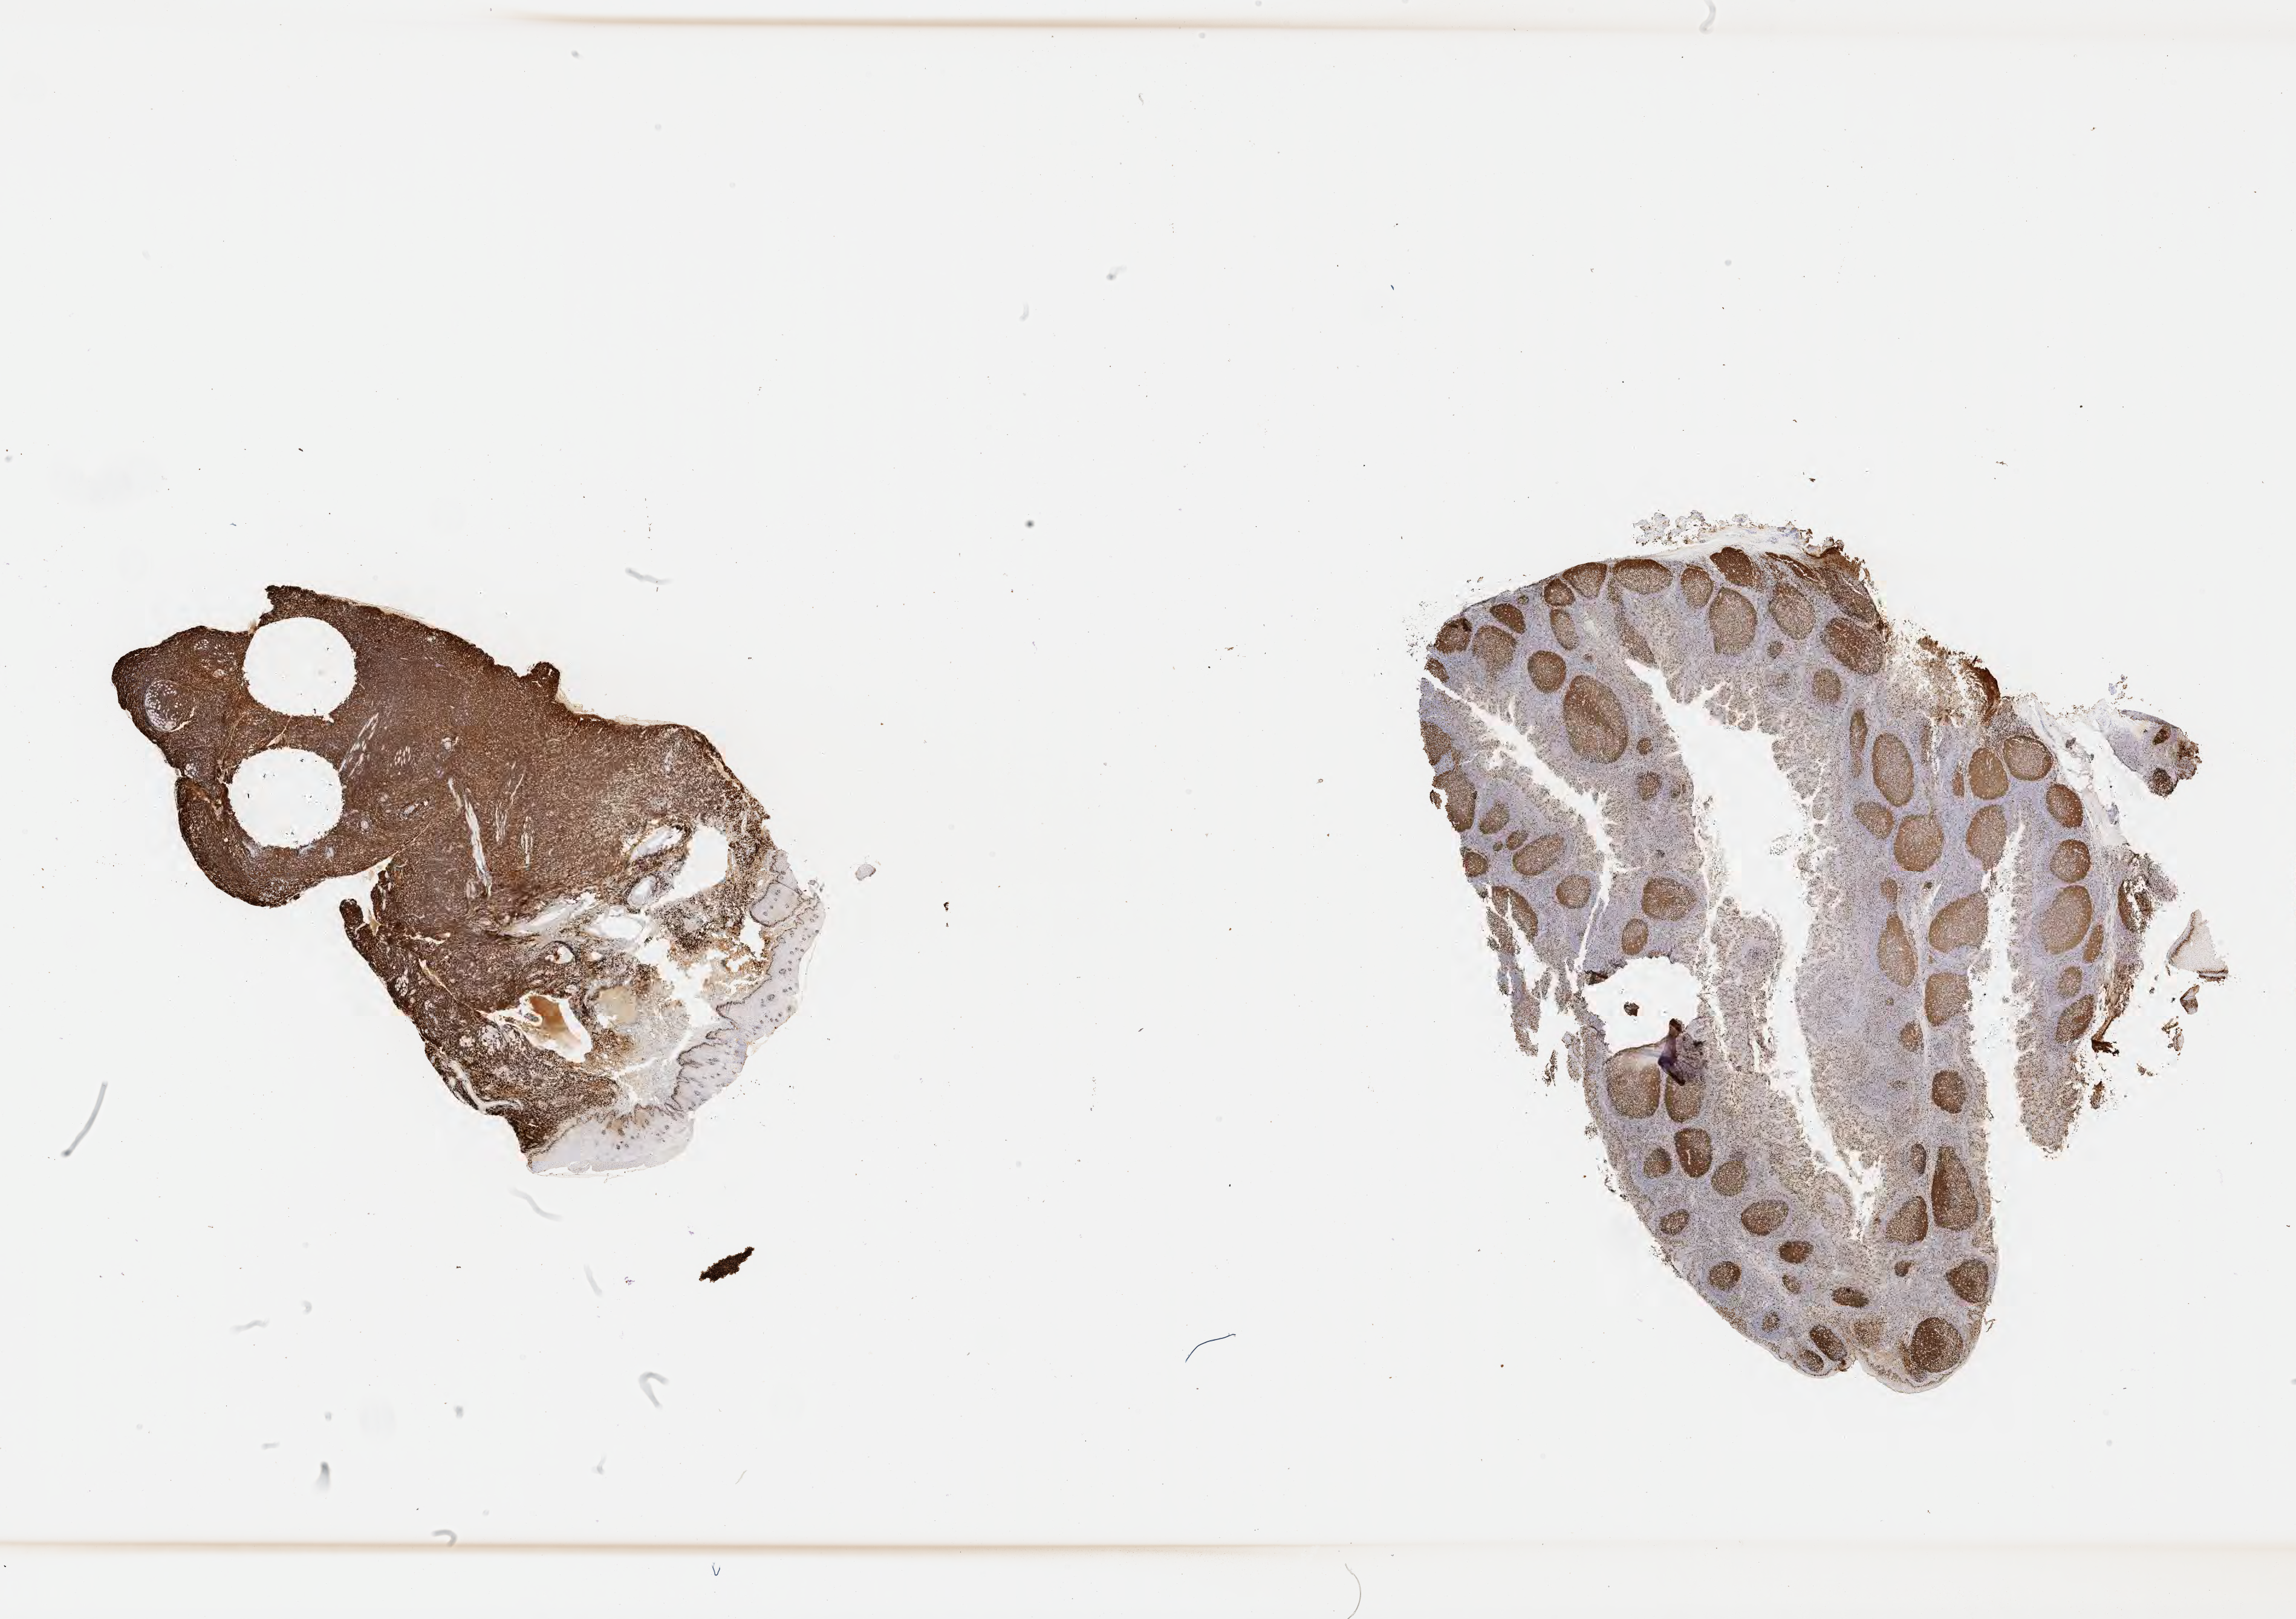
Immunohistochemistry (IHC) whole-slide image stained for Ki-67 — a low-resolution overview of the entire scanned area, about 30.7 x 21.6 mm; tumor tissue; anatomic site: cranium. Patient: male, age at initial diagnosis 6 years.
Diagnosis: Burkitt lymphoma, NOS.